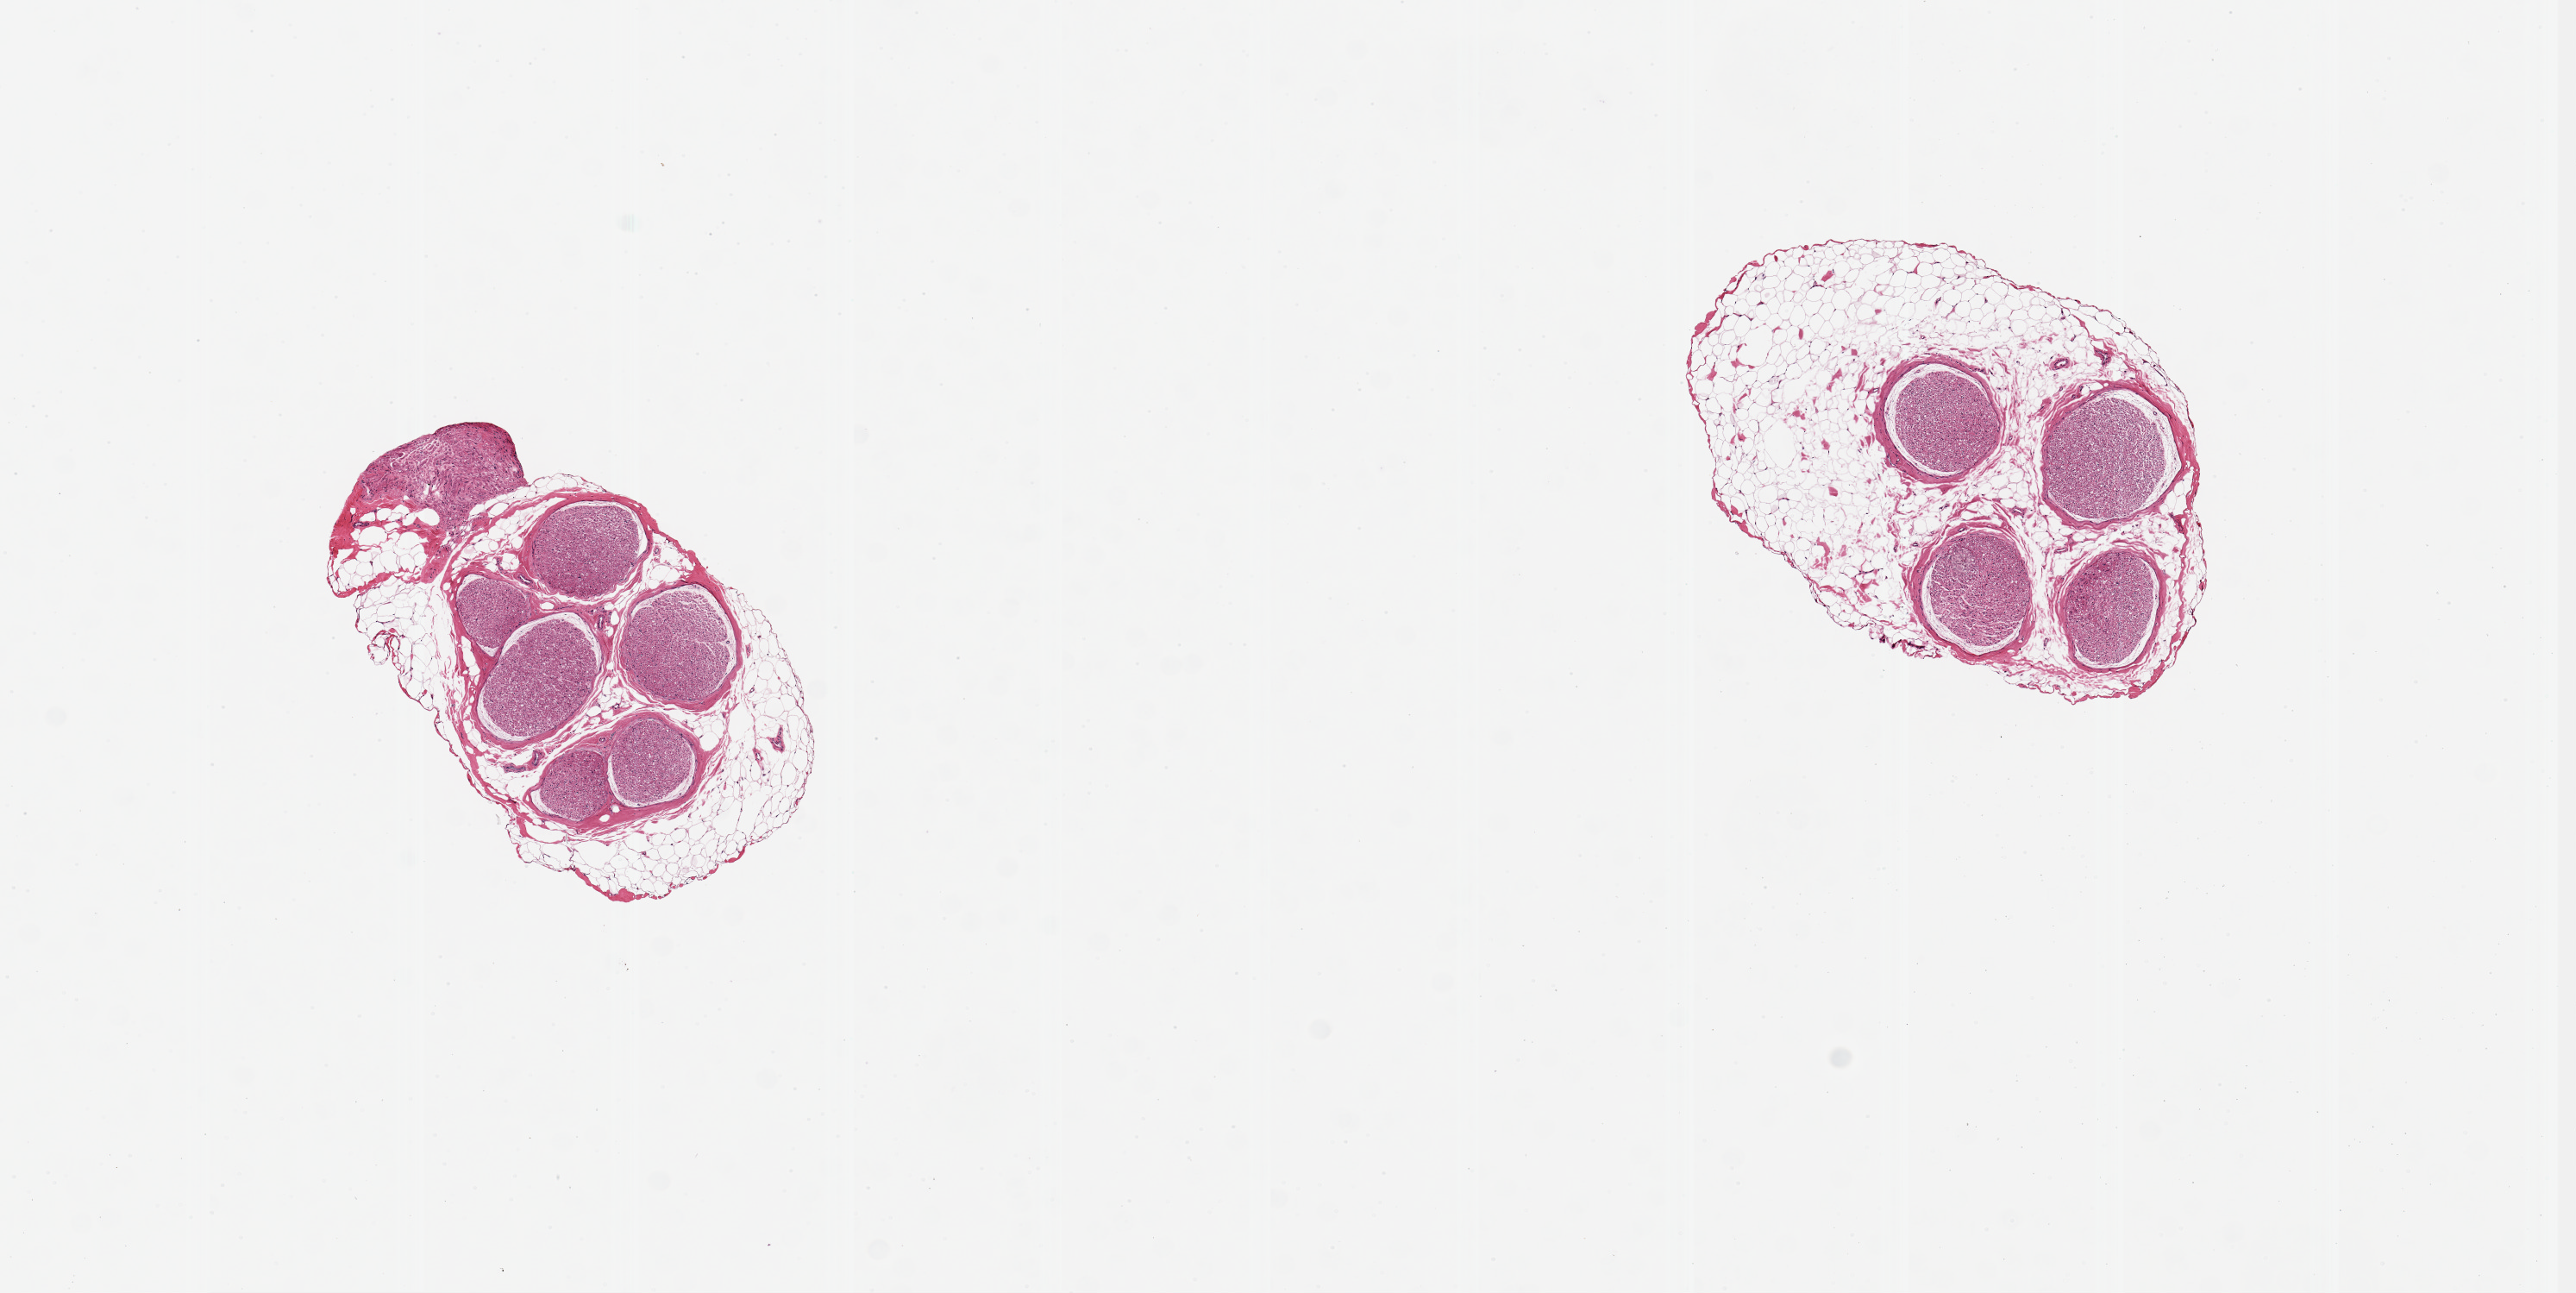
Whole-slide image, hematoxylin and eosin (H&E) stain, brightfield, low-resolution overview of the scanned area, about 11.8 x 5.9 mm (acquisition: 20x scan). PAXgene-fixed, paraffin-embedded tissue. Target tissue: tibial nerve. Donor tissue sample. Donor sex: female.
- review note (as recorded): 2 pieces 3x1 & 2x1 mm; ~30 to 50% surrounding adipose